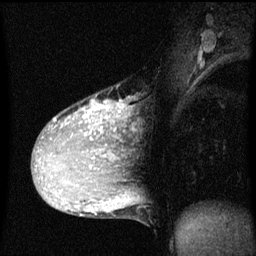
Breast MRI (dynamic contrast-enhanced), one sagittal slice. Slice 32 of 60 in the series (ordered by position). Dynamic contrast-enhanced series, image 2 of 3 at this slice position (ordered by acquisition). 1.5 T. TE 4.2 ms, TR 8 ms. 2 mm slice thickness. 256 × 256 image matrix. Patient: female, 36 years.
Annotated regions visible in this slice (semi-automatically segmented with operator editing):
- analysis volume of interest (the breast-tissue region the enhancement analysis was run in; not a lesion): bounding box <33,100,125,169> (left, top, right, bottom; pixels)
- tumour enhancement mask (voxels above the 70 % enhancement threshold inside the analysis volume of interest): <43,100,124,163>